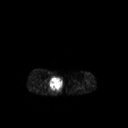
FDG PET of an extremity soft-tissue mass (from a PET/CT study), one axial slice; position 131 of 267 along the scan axis; 3.27 mm slice thickness; 128 × 128 image matrix, field of view 500 × 500 mm. Patient: male, 69 years. From the clinical record (not read from this slice): histological type: pleiomorphic liposarcoma; grade: high; site of the primary tumour: right calf.
Annotated regions visible in this slice (expert contour drawn on MRI and transferred to this co-registered scan by the dataset authors):
- gross tumour volume including surrounding oedema: bounding box [x1, y1, x2, y2] px = [49, 75, 63, 95]
- gross tumour volume (mass): [49, 76, 63, 91]